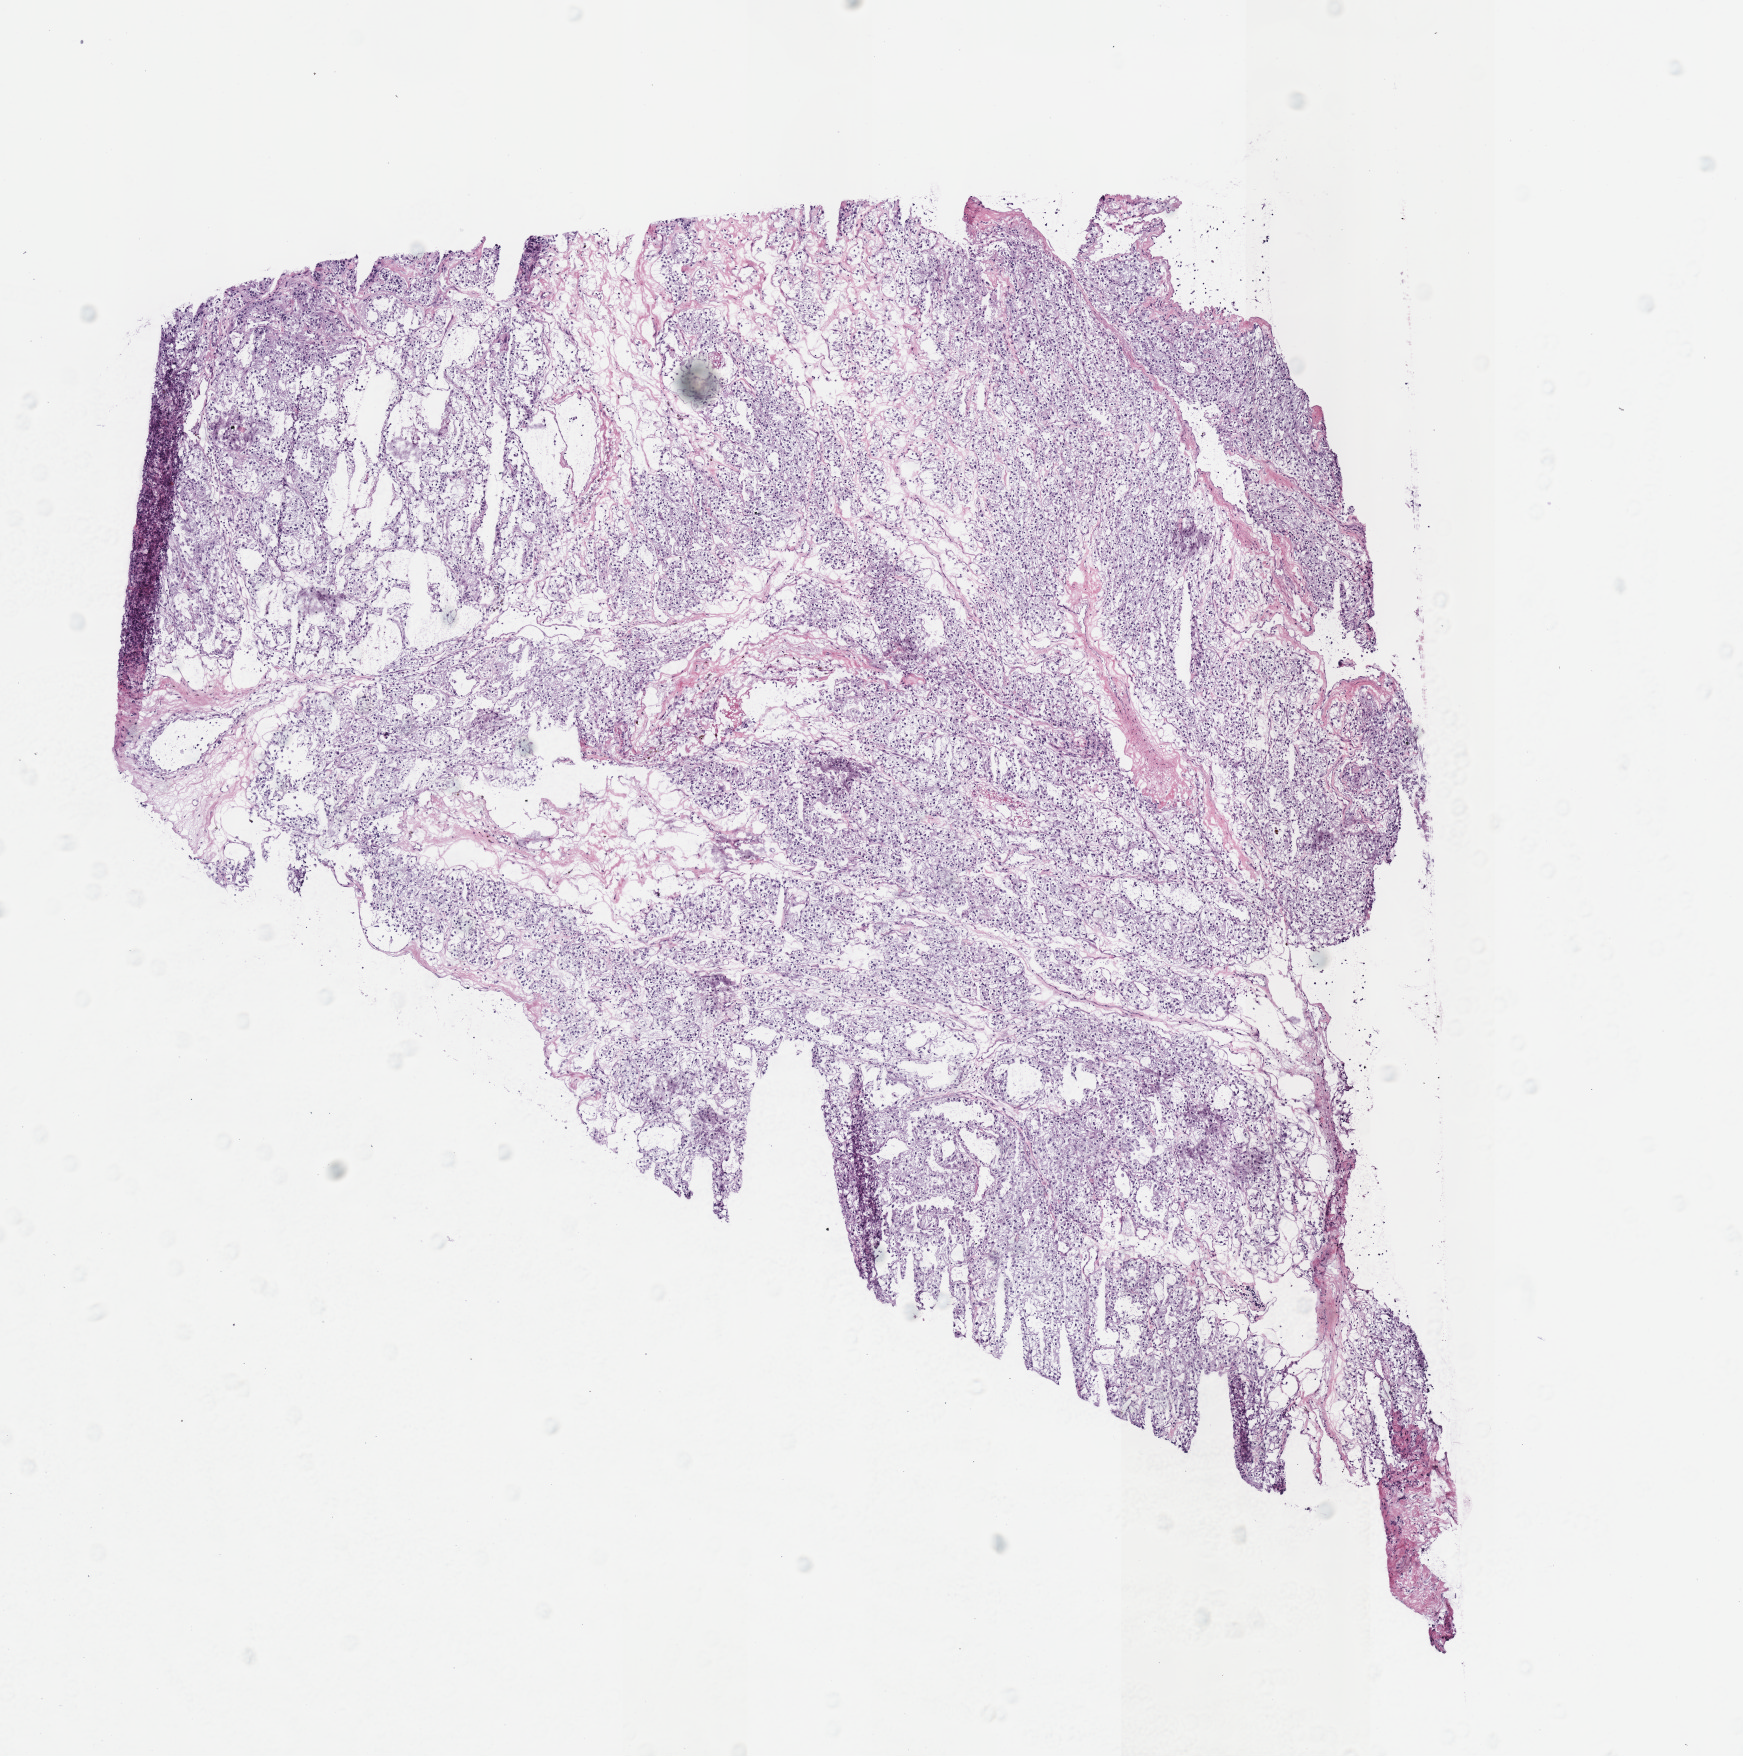
Whole-slide histology image, H&E-stained, whole scanned area (about 6.9 x 6.9 mm) shown as a low-resolution overview. Frozen section from the top of the tissue portion. Sample: primary tumour, kidney. Patient: male, age at initial diagnosis 53 years. Histologic grade: G3 (poorly differentiated). Pathologist review of this section (percent, as recorded): tumour cells 90%, tumour nuclei 85%, normal cells 0%, stromal cells 10%, necrosis 0%.
Diagnosis: Clear cell adenocarcinoma, NOS. TNM: T1b N0 M0. AJCC pathologic stage: I (7th edition).